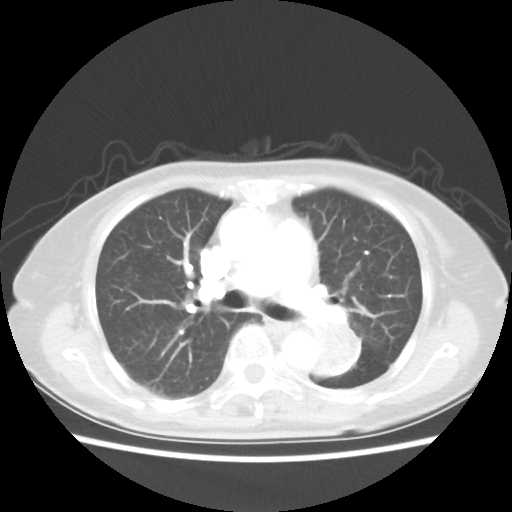
Chest CT, one axial slice; position 30 of 50 along the scan axis; 80 kVp; lung window (W 1500 / L -600 HU); 5 mm slice thickness; 512 × 512 image matrix, field of view 335 × 335 mm. Female patient, age 81 years. From the clinical record (not read from this slice): clinical TNM (as recorded): T2 N0 M1a.
Structures marked on this image (bounding box drawn by a radiologist):
- lung tumour (recorded histology: squamous cell carcinoma): bounding box [x1, y1, x2, y2] px = [307, 315, 375, 380]